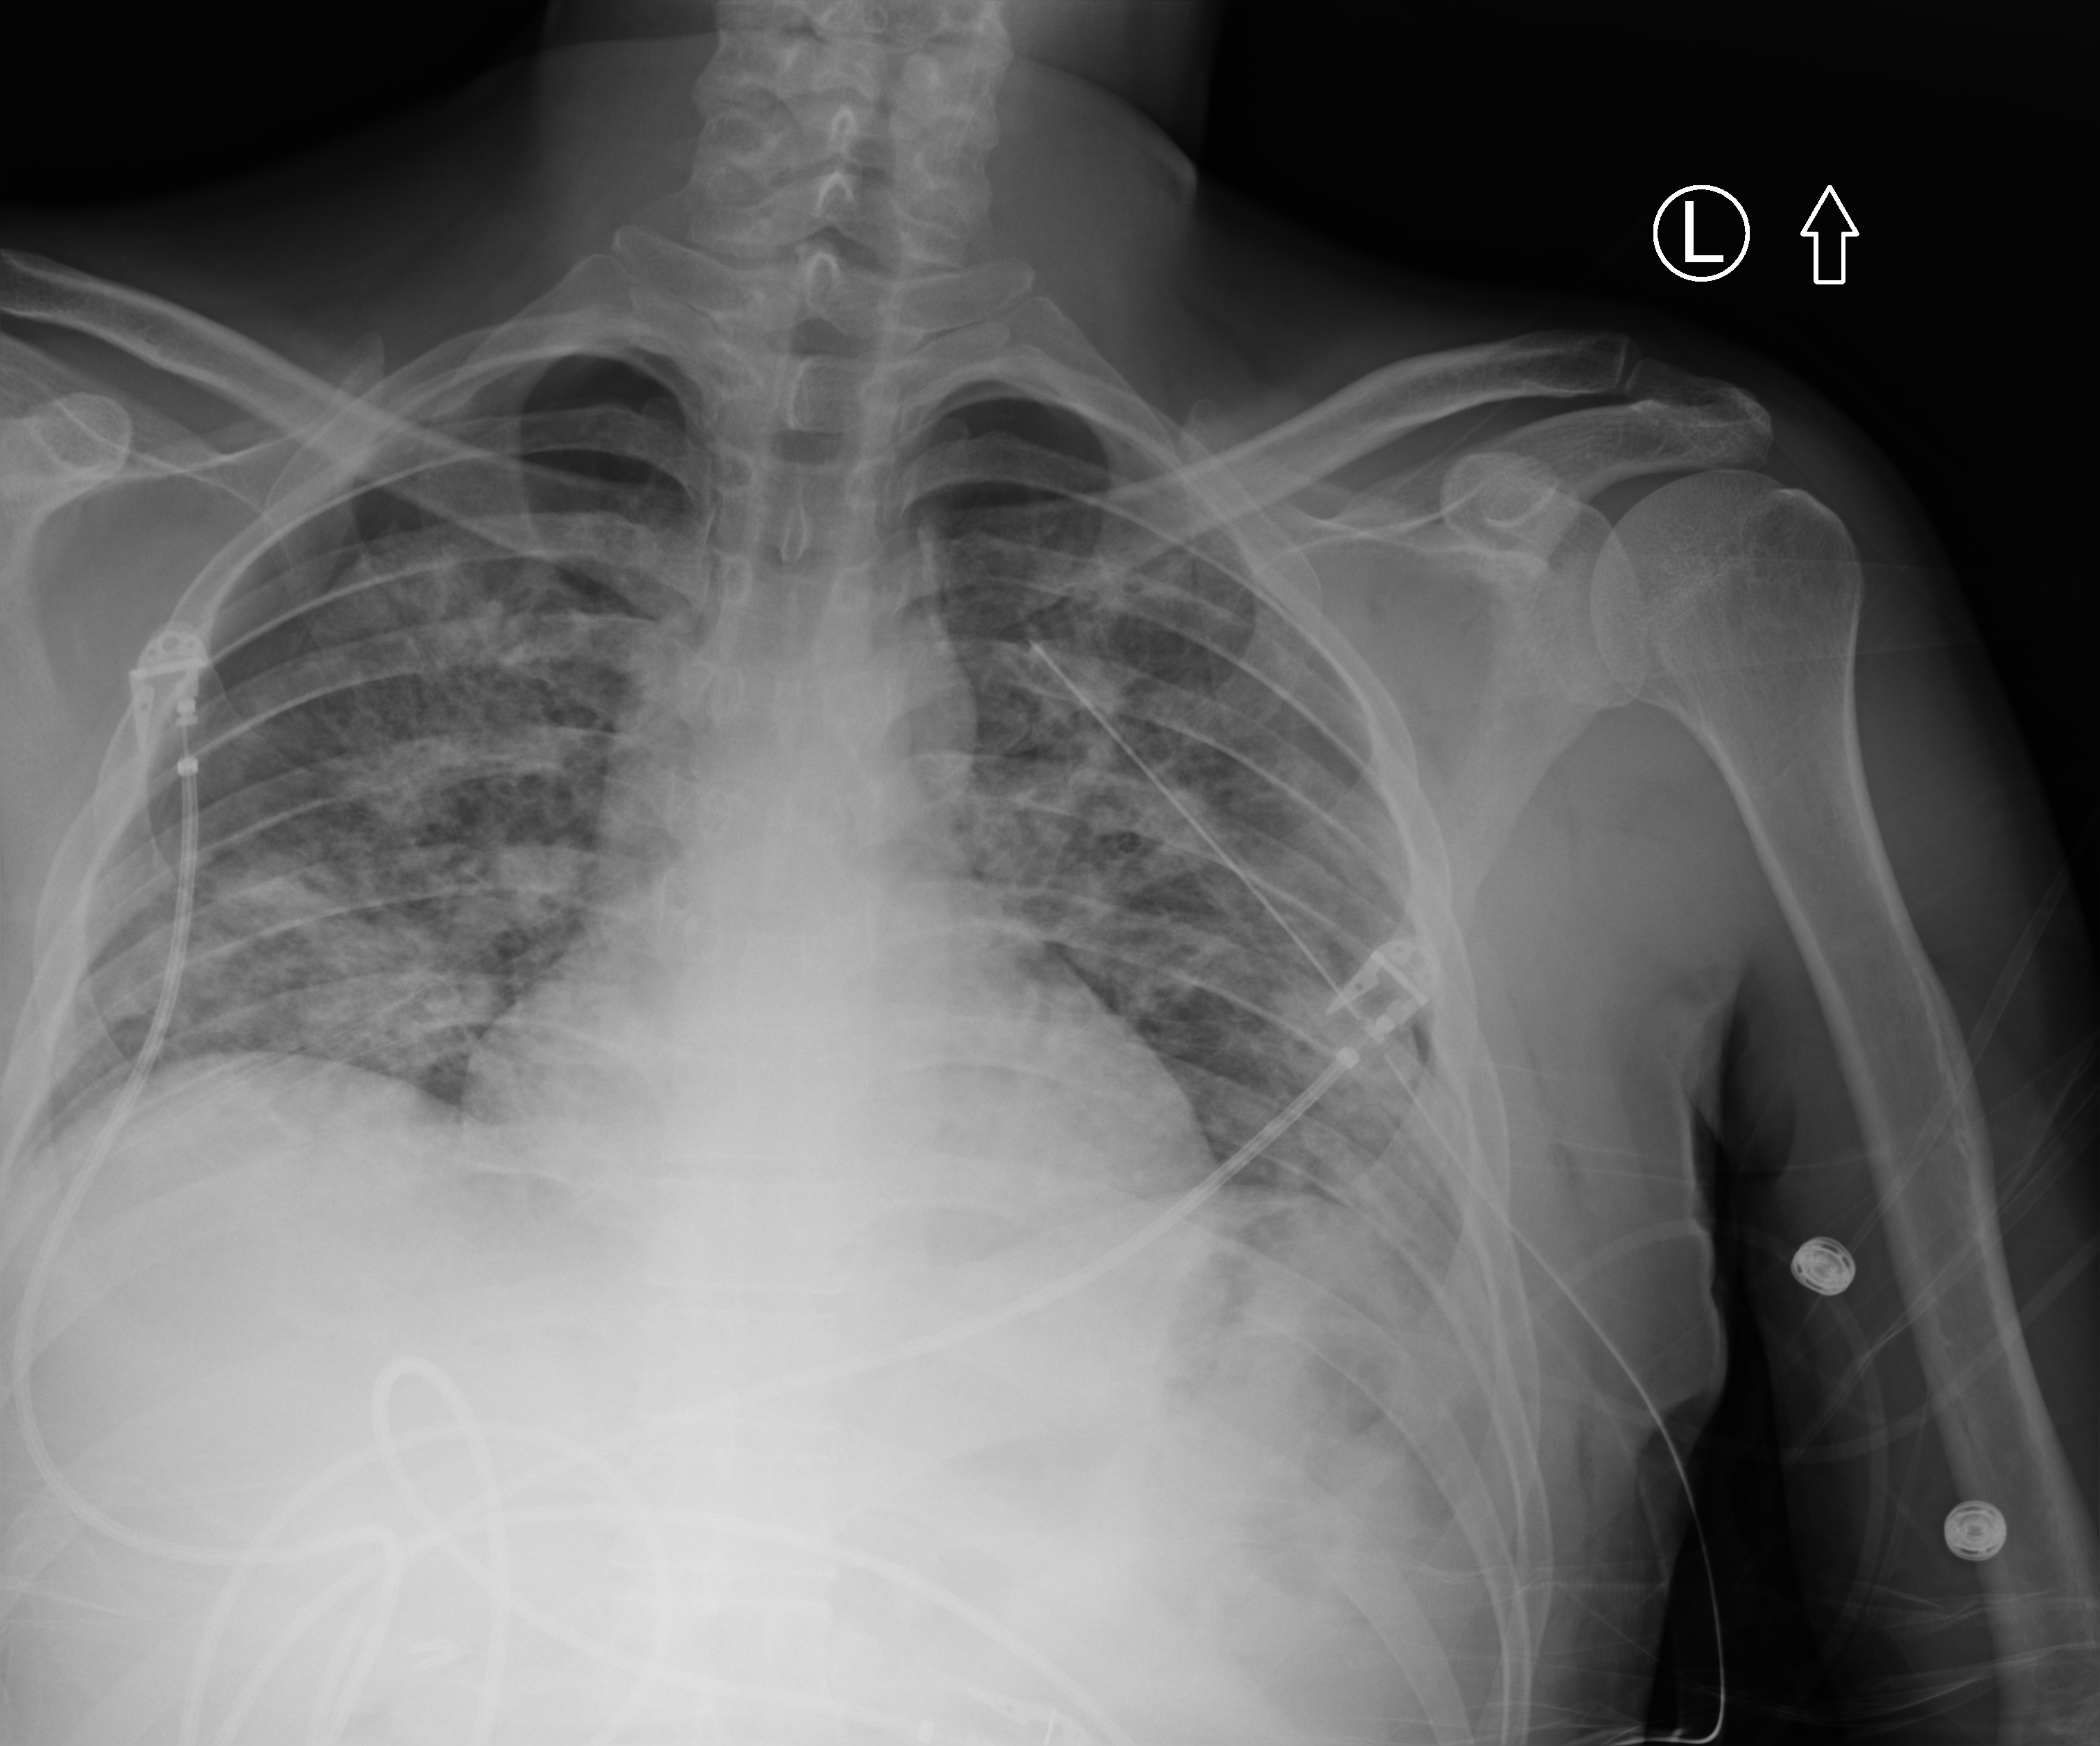
Chest X-ray (portable); anteroposterior (AP) projection. Patient hospitalised with COVID-19; male, aged 18–59 years.
From the hospital-stay record, not from the radiograph (when in the stay this image was taken is not recorded): COPD (admission record): no.